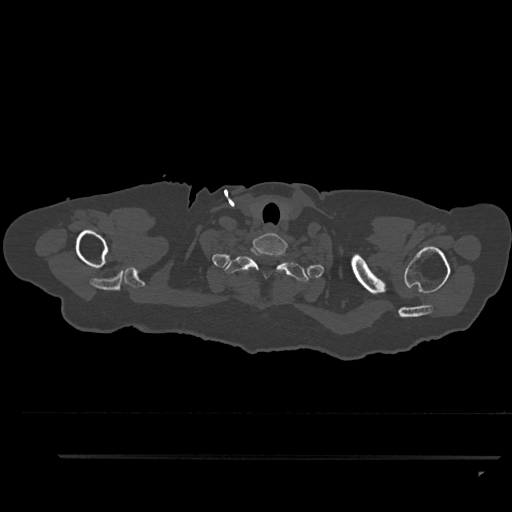
CT including the spine, one axial slice. Position 774 of 797 along the scan axis. Reconstruction kernel Br40s/3. 120 kVp. Bone window (W 1800 / L 400 HU). 512 × 512 image matrix, field of view 408 × 408 mm. Female patient, age 44 years. From the clinical record (not read from this slice): primary cancer: renal.
Structures marked on this image (semi-automatically segmented with operator editing):
- T1 vertebra: box from (x=224, y=246) to (x=309, y=282) px